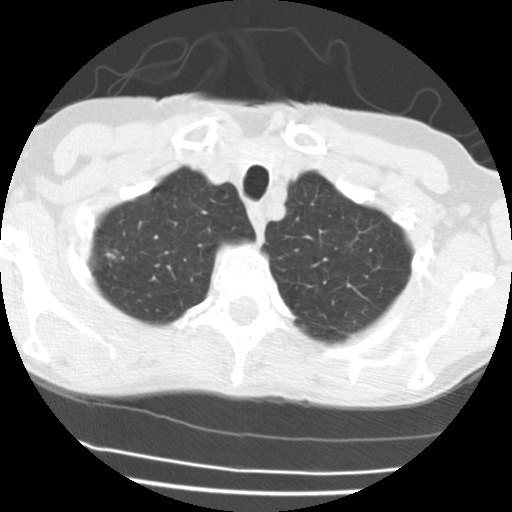
Chest CT (low-dose screening protocol), one axial image. Third annual screen. Lung window (W 1500 / L -600 HU). Slice 181 of 195 in the series. 512 × 512 image matrix. Female participant, aged 58 years at enrolment. Current smoker at enrolment.
- Expert reader's lesion annotation, bounding box (x1, y1, x2, y2) in pixels: (85, 238, 123, 278).
- The screening reader recorded 3 non-calcified nodules or masses ≥4 mm on this exam (right upper lobe, left upper lobe, right upper lobe); which of them this box marks is not recorded.
- Lung cancer was diagnosed 153 days after this screen: bronchiolo-alveolar adenocarcinoma, NOS, right upper lobe, well differentiated (G1), stage IA (AJCC 6th edition), 8 mm at pathology.